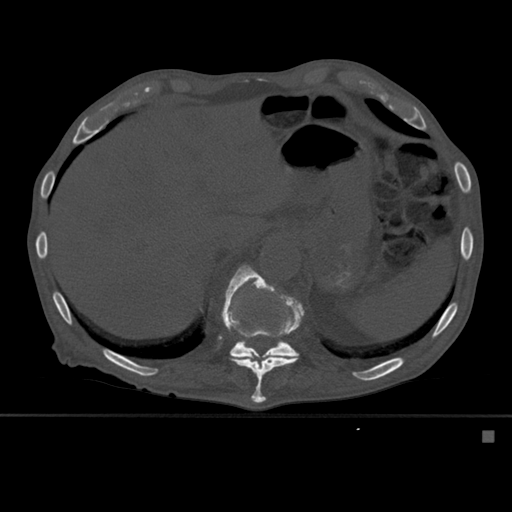
CT including the spine, one axial slice. Position 287 of 527 along the scan axis. Bone window (W 1800 / L 400 HU). 1.5 mm slice thickness. 512 × 512 image matrix, field of view 373 × 373 mm. Male patient, age 78 years. From the clinical record (not read from this slice): primary cancer: prostate.
Annotated regions visible in this slice (semi-automatic segmentation, software-assisted and operator-edited):
- T11 vertebra: bounding box [x1, y1, x2, y2] px = [222, 265, 304, 404]
- T12 vertebra: [224, 278, 302, 359]